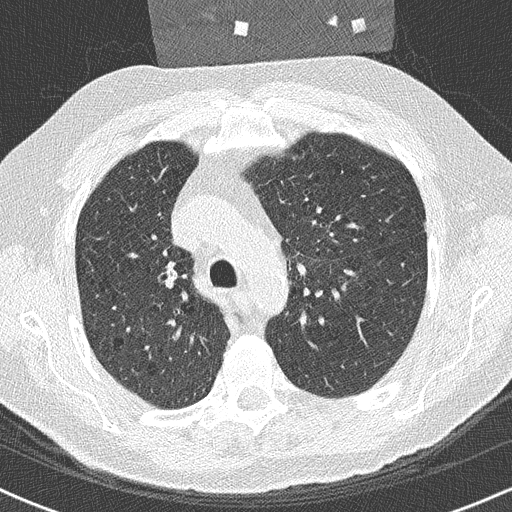
Low-dose screening chest CT, axial slice. First (baseline) screen. Lung window (W 1500 / L -600 HU). 2 mm slice thickness. Lung (sharp) reconstruction kernel (B50f). Male participant, aged 59 years at enrolment. Former smoker at enrolment.
Lesion marked by an expert reader, bounding box <147,256,180,293> (left, top, right, bottom; pixels). No non-calcified nodule or mass ≥4 mm was recorded by the screening reader at this exam. Official screen result: negative screen, minor abnormalities not suspicious for lung cancer. Lung cancer was diagnosed 360 days after this screen (after the second annual screen): squamous cell carcinoma, NOS, right upper lobe, poorly differentiated (G3), stage IIA (AJCC 6th edition), 20 mm at pathology.